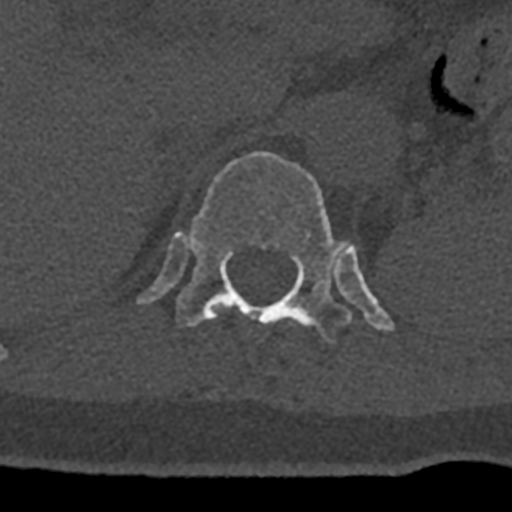
CT including the spine, one axial slice. Position 501 of 797 along the scan axis. Bone window (W 1800 / L 400 HU). 0.5 mm slice thickness. 512 × 512 image matrix, field of view 160 × 160 mm. Patient: male, 74 years. Case-level facts recorded for this patient, not image findings: primary cancer: renal; vertebrae with lytic lesions (as recorded): T10, L1, L2, L3, L4, L5.
Annotated regions visible in this slice (semi-automatically segmented with operator editing):
- T11 vertebra: bounding box <215,307,221,315> (left, top, right, bottom; pixels)
- T12 vertebra: <136,151,394,344>